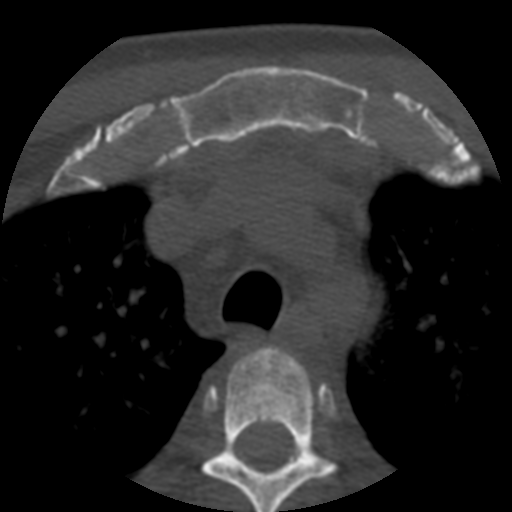
CT including the spine, one axial slice; position 413 of 508 along the scan axis; reconstruction kernel STANDARD; 120 kVp; bone window (W 1800 / L 400 HU); 1.25 mm slice thickness; 512 × 512 image matrix. Patient age 57 years. Case-level facts recorded for this patient, not image findings: primary cancer: prostate.
Annotated regions visible in this slice (semi-automatically segmented with operator editing):
- T3 vertebra: bounding box (x1, y1, x2, y2) in pixels: (201, 346, 335, 512)